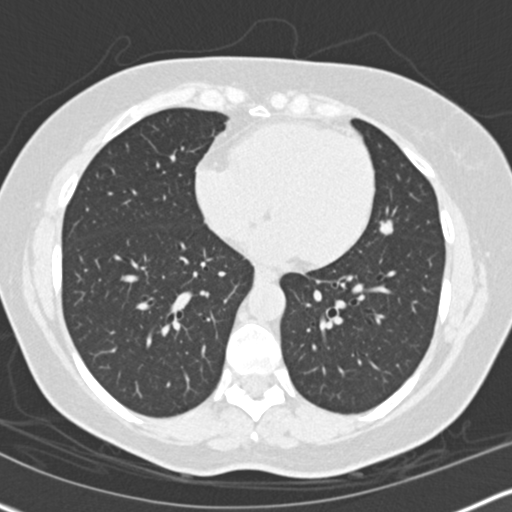
Chest CT (low-dose screening protocol), one axial image; second annual screen; lung window (W 1500 / L -600 HU); slice 93 of 158 in the series. Female participant, aged 56 years at enrolment.
Expert-annotated lung lesion, bounding box (x1, y1, x2, y2) in pixels: (360, 202, 408, 249). Reader record for this screening exam (exam-level; its link to the box is not recorded): non-calcified nodule or mass ≥4 mm, lingula, 10 × 8 mm, smooth margins, soft tissue attenuation, pre-existing on the prior screen: yes; interval growth: yes. Official screen result: positive, other. Lung cancer was diagnosed 506 days after this screen (after the third annual screen): adenocarcinoma, NOS, left upper lobe, poorly differentiated (G3), stage IIIA (AJCC 6th edition), 15 mm at pathology.